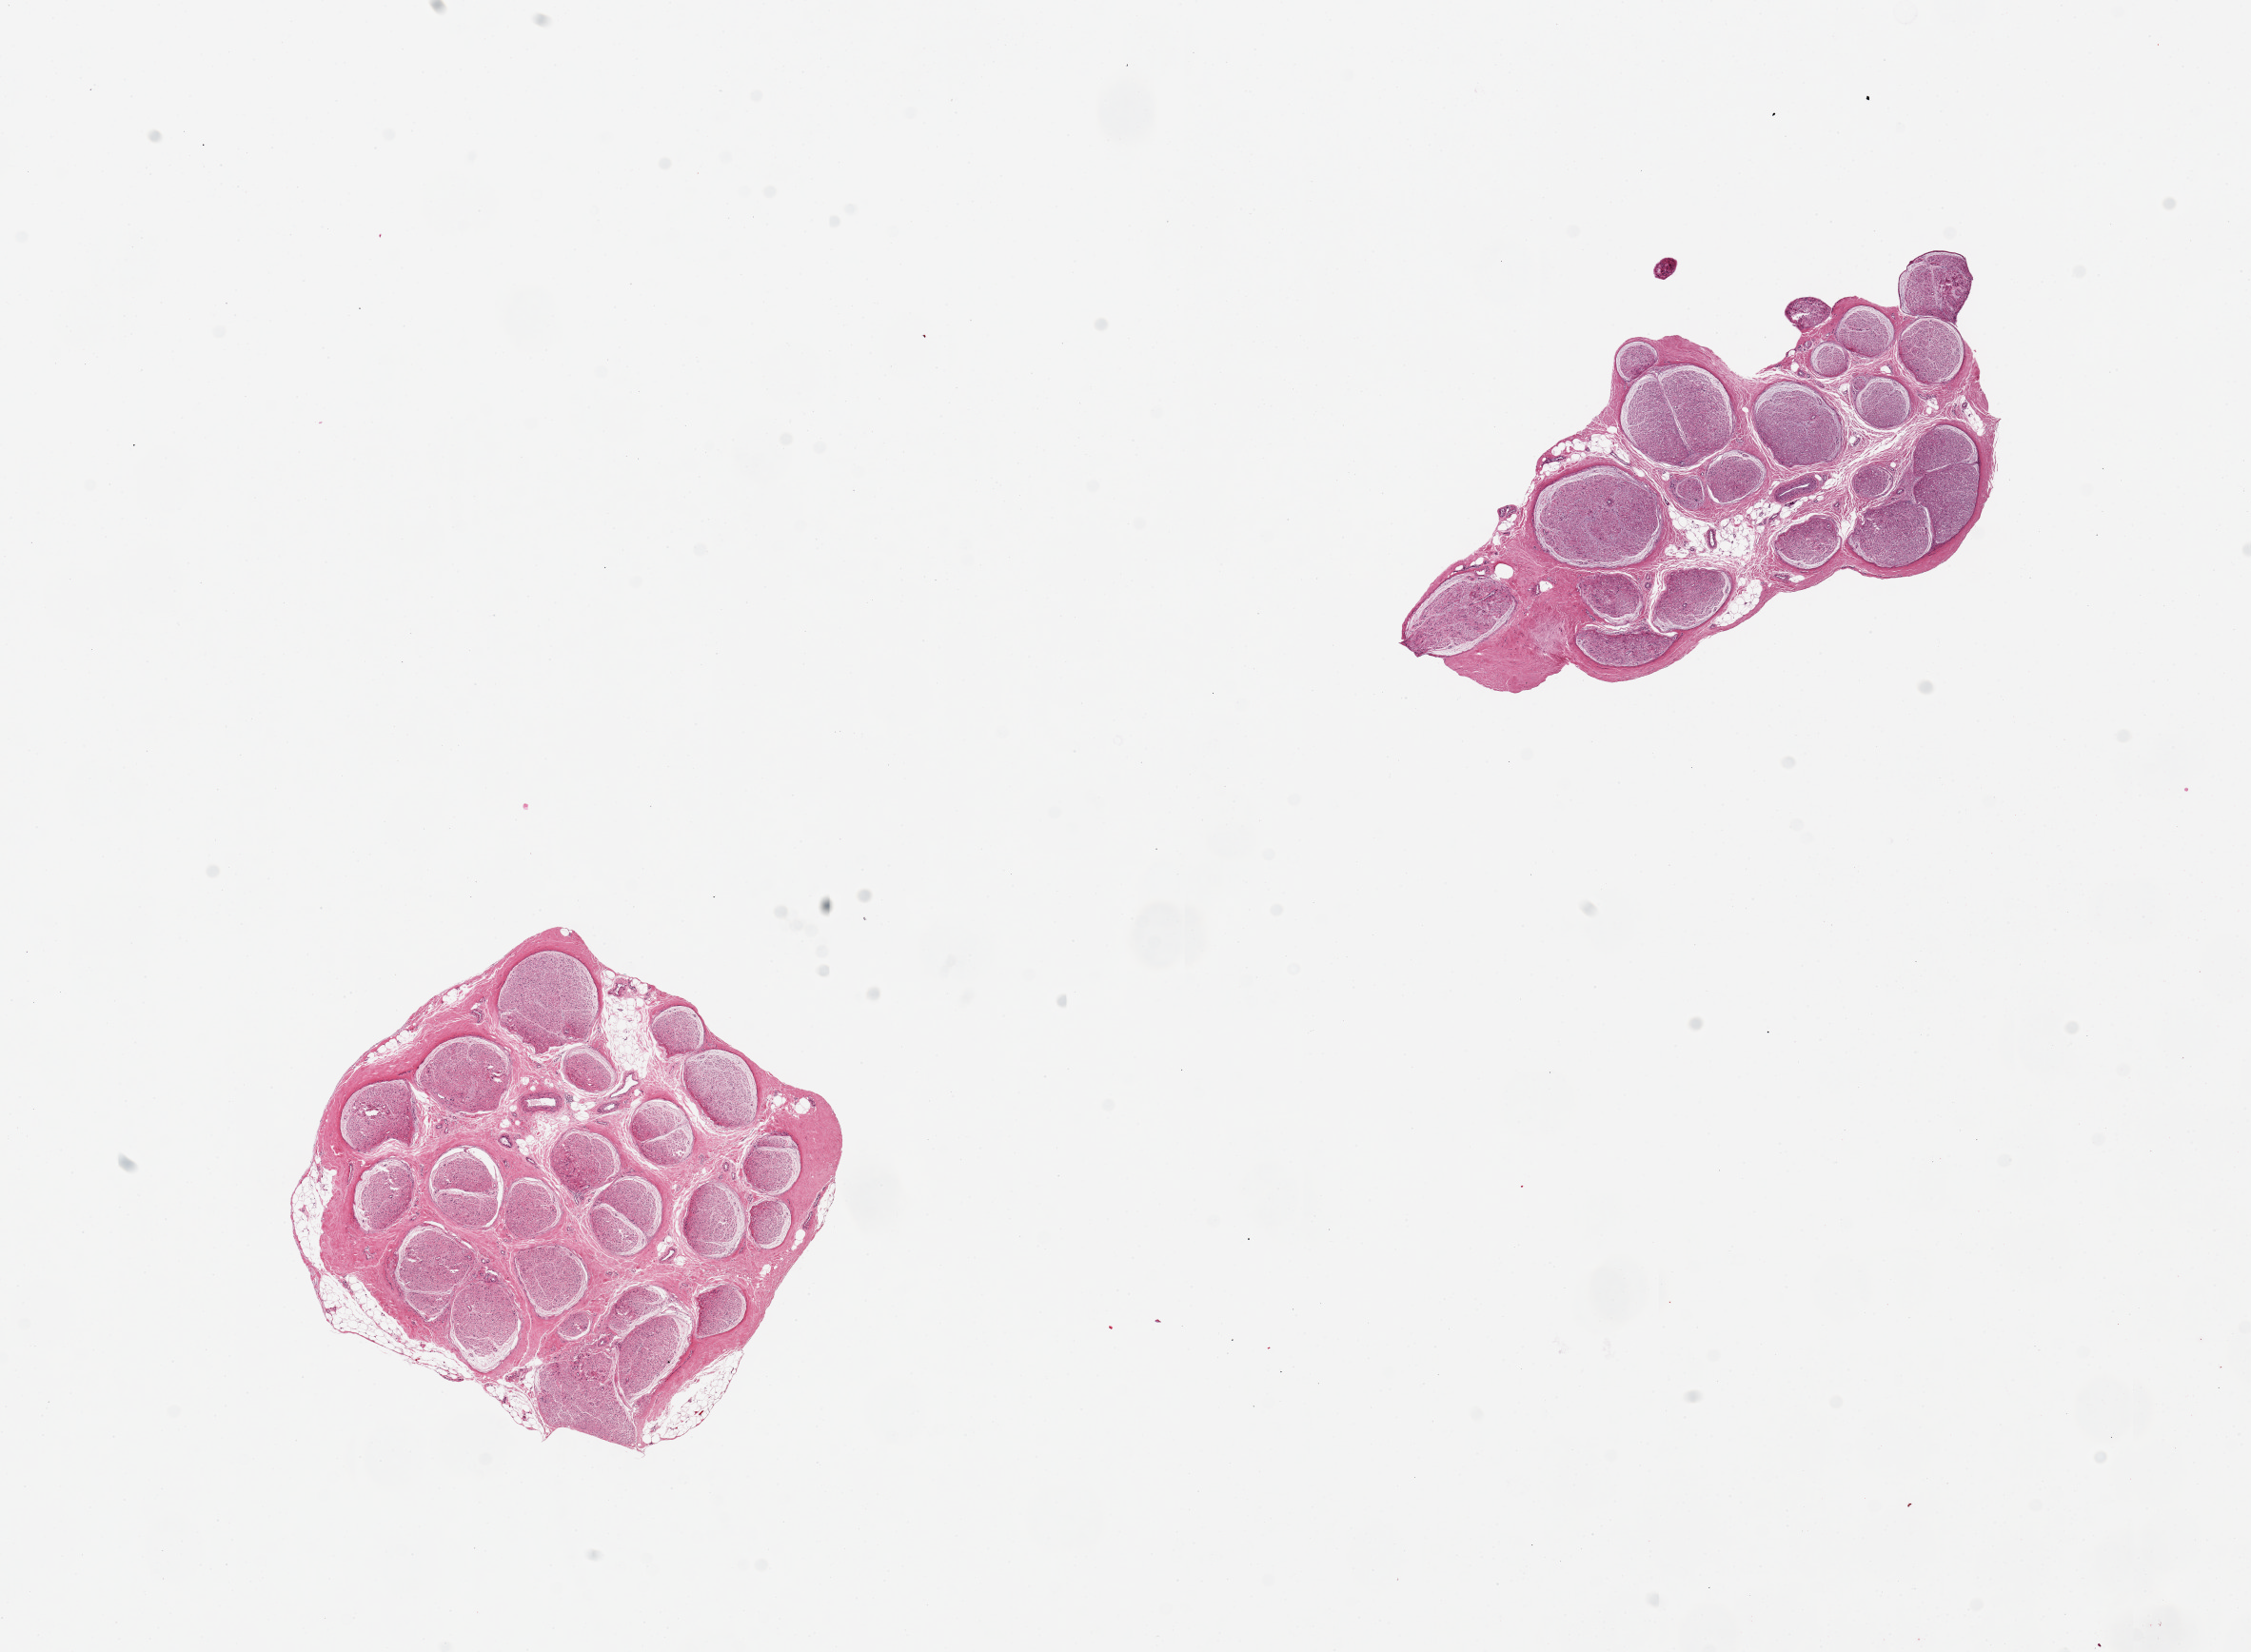
Hematoxylin and eosin (H&E) whole-slide image, a low-resolution overview of the entire scanned area, about 18.7 x 13.7 mm, PAXgene-fixed, paraffin-embedded tissue, section of tibial nerve (target tissue), donor tissue sample. Male donor.
• review note (as recorded): 2 pieces, good clean specimens, trace minute nubbins of fat on one aliquot, ~0.3mm